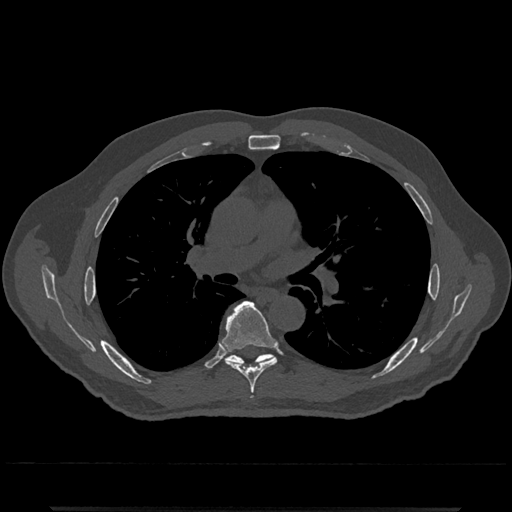
CT including the spine, one axial slice. Position 758 of 797 along the scan axis. Reconstruction kernel Br40s/3. 120 kVp. Bone window (W 1800 / L 400 HU). 0.5 mm slice thickness. 512 × 512 image matrix, field of view 393 × 393 mm. Male patient, age 67 years. From the clinical record (not read from this slice): primary cancer: prostate.
Annotated regions visible in this slice (semi-automatic segmentation, software-assisted and operator-edited):
- T6 vertebra: bounding box [x1, y1, x2, y2] px = [223, 301, 277, 400]
- T7 vertebra: [227, 354, 273, 365]